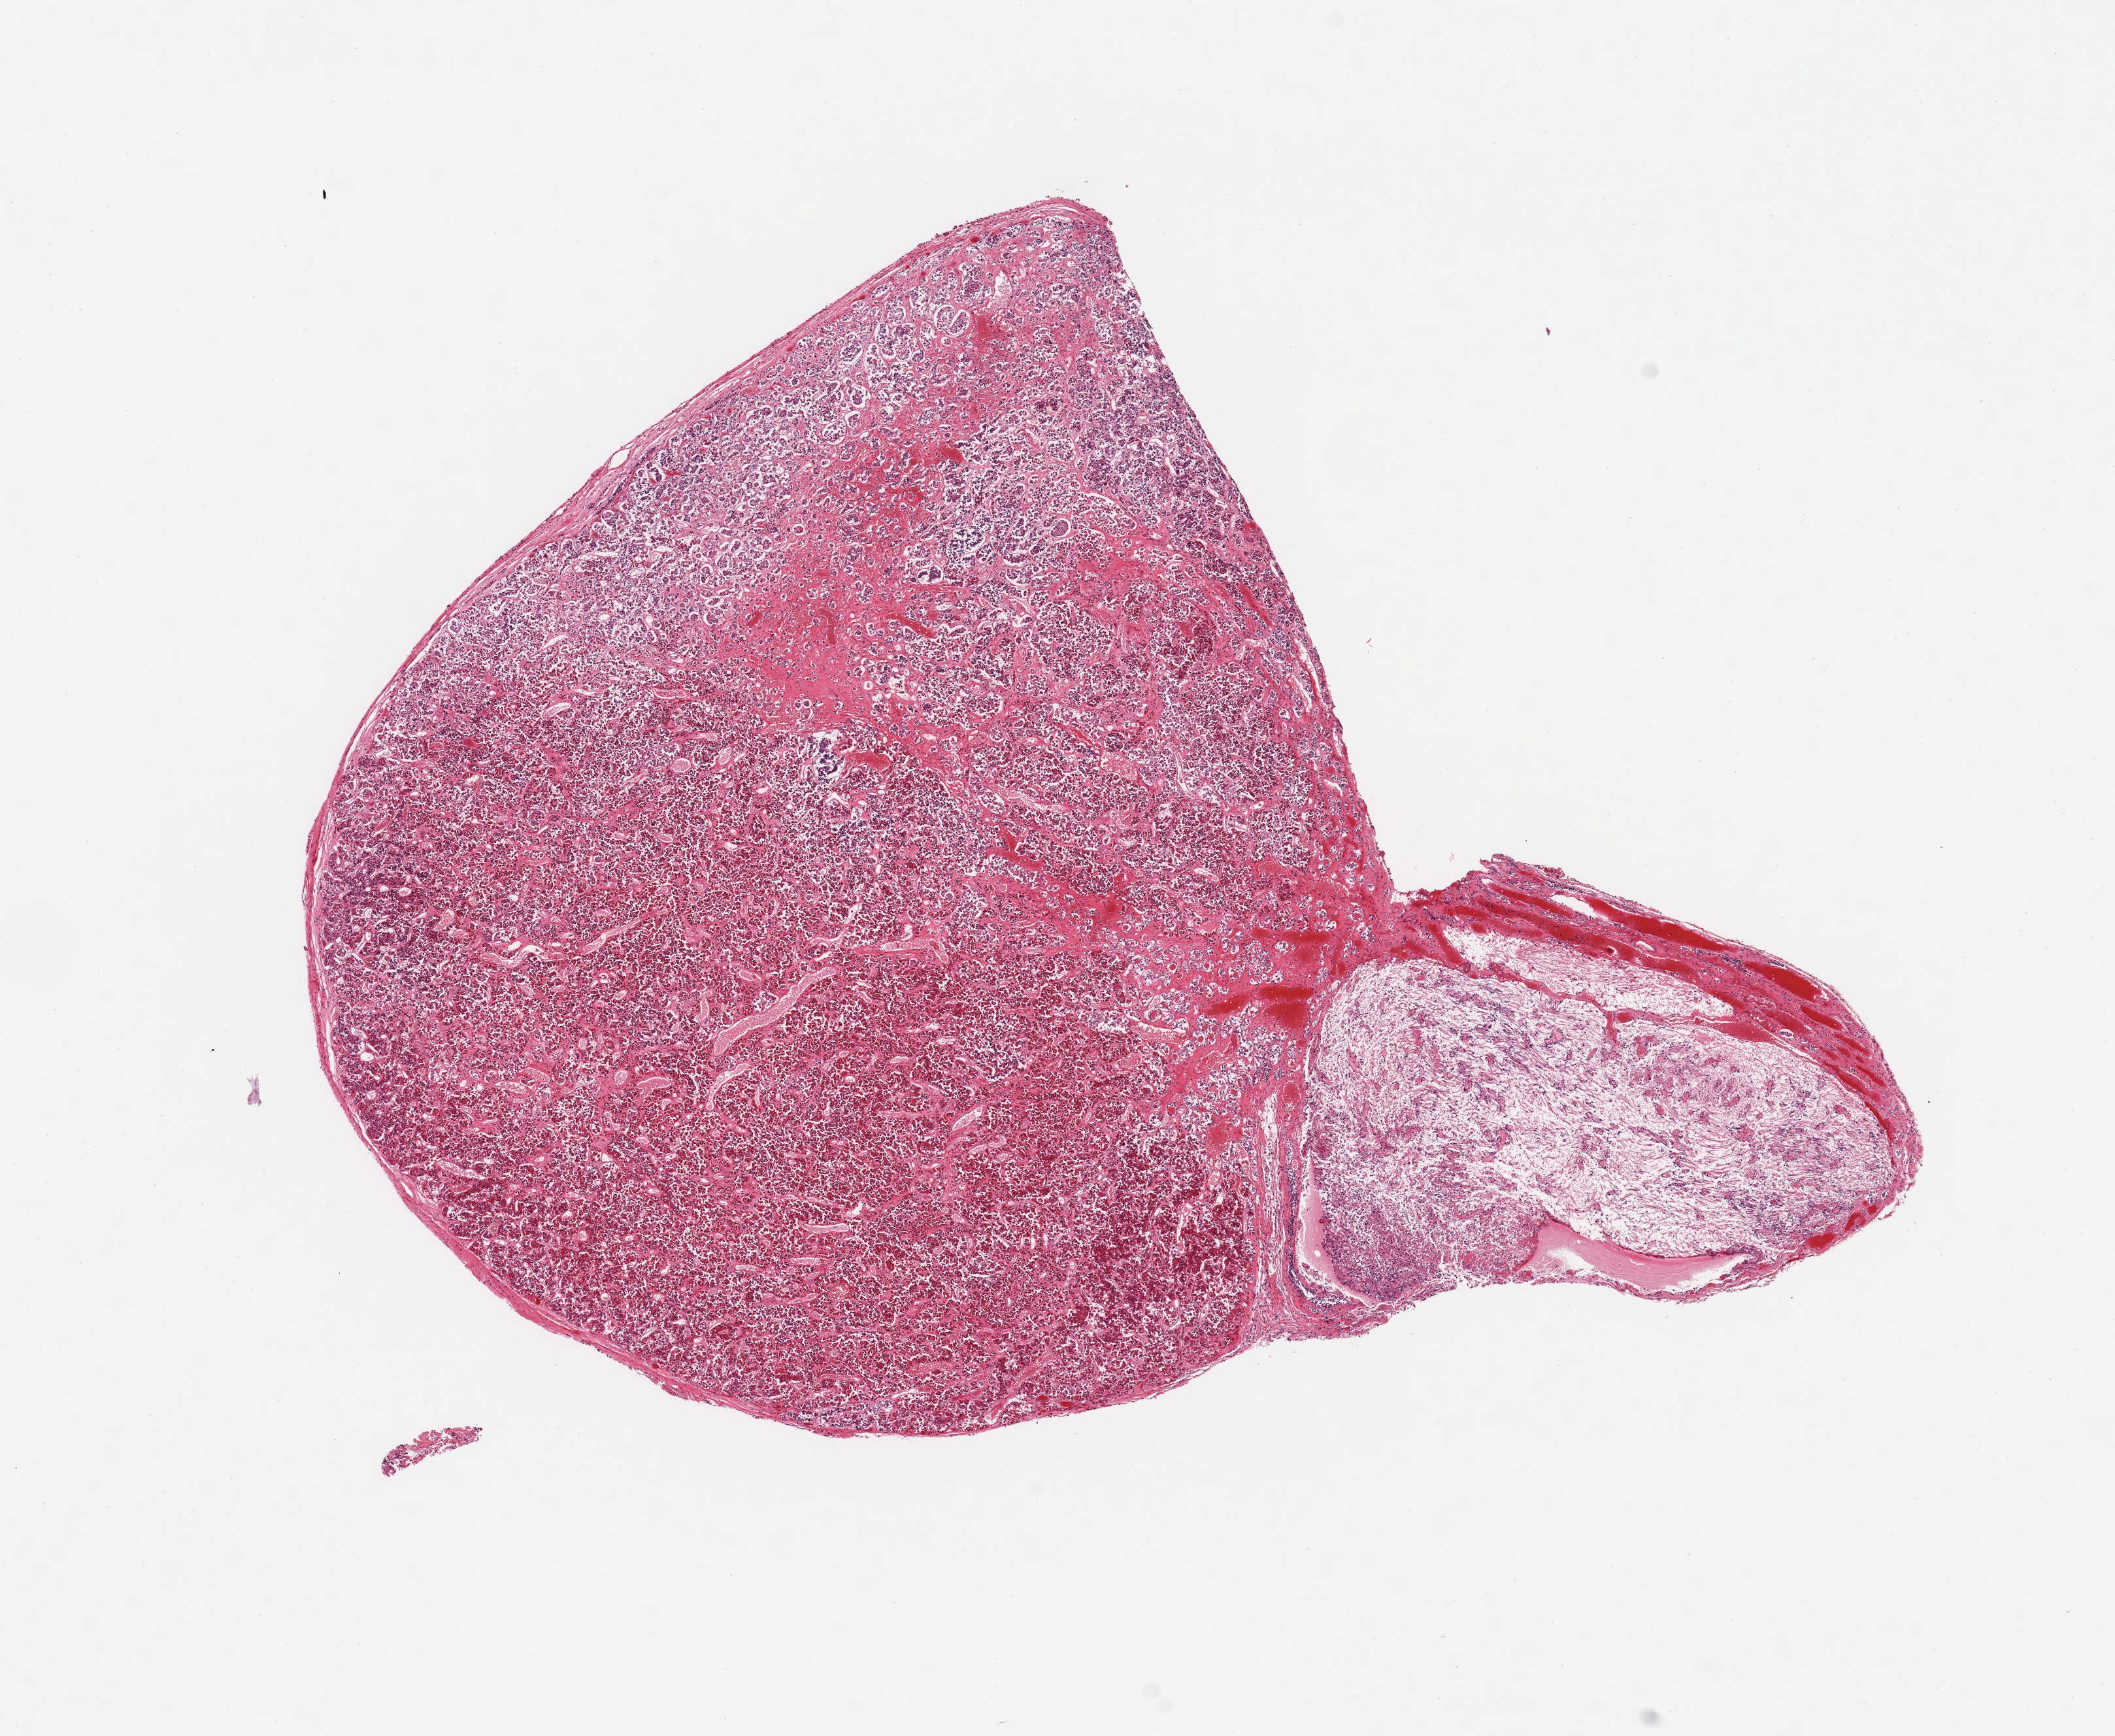
H&E whole-slide image, brightfield — shown as a low-resolution overview of the whole scanned area (about 12.8 x 10.5 mm, acquisition: 20x scan); PAXgene-fixed paraffin-embedded (PFPE) section; target tissue: pituitary; tissue donor sample. Male donor.
* review note (as recorded): 1 piece; moderately autolyzed adenohypophysis (75% tissue) and neurohypophysis (25% tissue)